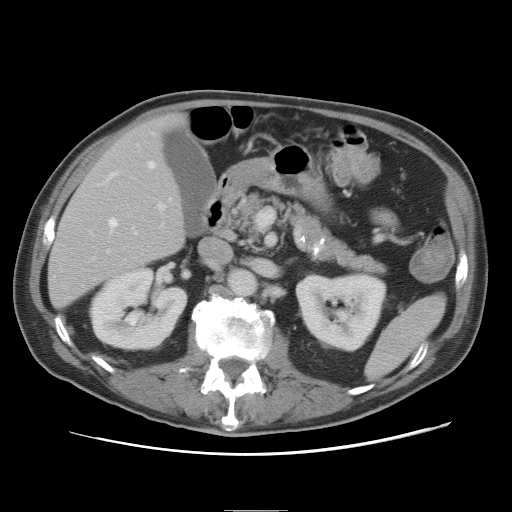
Contrast-enhanced abdominal CT, one axial slice. Slice 34 of 89 in the series (ordered by position). 120 kVp. Intravenous contrast given. Soft-tissue window (W 400 / L 40 HU). 512 × 512 image matrix, field of view 375 × 375 mm. Male patient, age 69 years. From the clinical record (not read from this slice): diagnosis: colorectal cancer liver metastases, imaged before liver resection; multiple liver metastases: no; largest metastasis: 8.5 cm; disease in both lobes: no.
Structures marked on this image (outlined manually by an expert reader):
- hepatic veins: box from (x=108, y=161) to (x=172, y=234) px
- liver: (x=49, y=117)–(x=185, y=307)
- planned liver remnant (the part of the liver to remain after resection): (x=49, y=116)–(x=185, y=307)
- portal vein (with intrahepatic branches): (x=108, y=202)–(x=166, y=252)